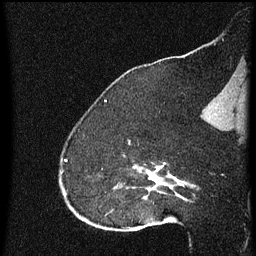
Breast MRI (dynamic contrast-enhanced), one sagittal slice; position 45 of 60 along the scan axis; dynamic contrast-enhanced series, image 2 of 4 at this slice position (ordered by acquisition); 1.5 T; TE 4.2 ms, TR 8 ms; 2 mm slice thickness; 256 × 256 image matrix. Patient: female, 52 years.
Structures marked on this image (semi-automatically segmented with operator editing):
- analysis volume of interest (the breast-tissue region the enhancement analysis was run in; not a lesion): bounding box [x1, y1, x2, y2] px = [73, 154, 172, 219]
- tumour enhancement mask (voxels above the 70 % enhancement threshold inside the analysis volume of interest): [135, 164, 172, 199]